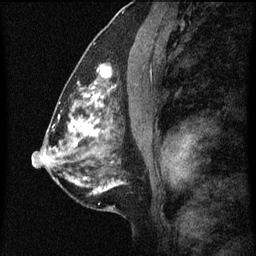
Breast MRI (dynamic contrast-enhanced), one sagittal slice. Position 32 of 60 along the scan axis. Dynamic contrast-enhanced series, image 2 of 7 at this slice position (ordered by acquisition). 1.5 T. TE 4.2 ms, TR 8 ms. 256 × 256 image matrix, field of view 180 × 180 mm. Female patient, age 51 years.
Structures marked on this image (semi-automatically segmented with operator editing):
- analysis volume of interest (the breast-tissue region the enhancement analysis was run in; not a lesion): bounding box (x1, y1, x2, y2) in pixels: (86, 48, 122, 101)
- tumour enhancement mask (voxels above the 70 % enhancement threshold inside the analysis volume of interest): (86, 68, 112, 101)